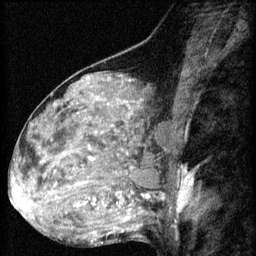
Breast MRI (dynamic contrast-enhanced), one sagittal slice. Position 34 of 60 along the scan axis. 3 images stored at this slice position (order not interpretable as contrast timing). 1.5 T. TE 4.2 ms, TR 8.2 ms. 2 mm slice thickness. 256 × 256 image matrix. Female patient, age 48 years.
Outlined on this slice (semi-automatic segmentation, software-assisted and operator-edited):
- analysis volume of interest (the breast-tissue region the enhancement analysis was run in; not a lesion): box from (x=48, y=160) to (x=125, y=217) px
- tumour enhancement mask (voxels above the 70 % enhancement threshold inside the analysis volume of interest): (x=77, y=200)–(x=96, y=207)